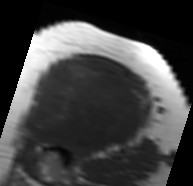
MRI of an extremity soft-tissue mass, one axial slice; position 50 of 91 along the scan axis; MR volume resampled by the dataset authors to the PET/CT grid (not the native acquisition matrix); 193 × 186 image matrix, field of view 188 × 182 mm. Female patient. From the clinical record (not read from this slice): histological type: malignant solitary fibrous tumor; grade: intermediate; site of the primary tumour: right thigh.
Outlined on this slice (expert contour drawn on MRI and transferred to this co-registered scan by the dataset authors):
- gross tumour volume including surrounding oedema: bounding box (x1, y1, x2, y2) in pixels: (19, 58, 148, 152)
- gross tumour volume (mass): (24, 58, 144, 150)